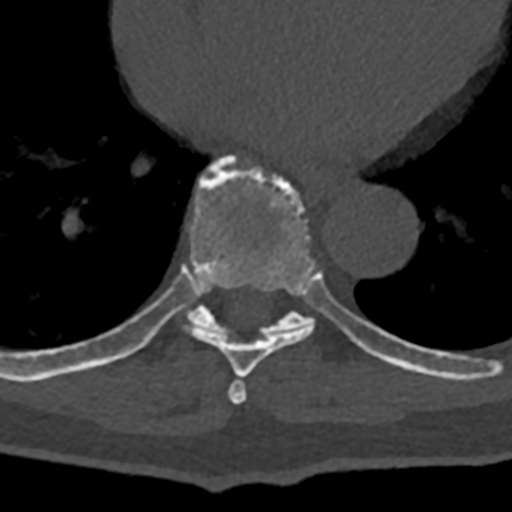
CT including the spine, one axial slice. Slice 691 of 797 in the series (ordered by position). Reconstruction kernel Br40s/3. 120 kVp. Bone window (W 1800 / L 400 HU). 512 × 512 image matrix, field of view 160 × 160 mm. Male patient, age 74 years. Case-level facts recorded for this patient, not image findings: primary cancer: renal; vertebrae with lytic lesions (as recorded): T10, L1, L2, L3, L4, L5.
Outlined on this slice (semi-automatic segmentation, software-assisted and operator-edited):
- T7 vertebra: bounding box <228,377,247,404> (left, top, right, bottom; pixels)
- T8 vertebra: <70,155,386,377>
- T9 vertebra: <104,266,432,376>